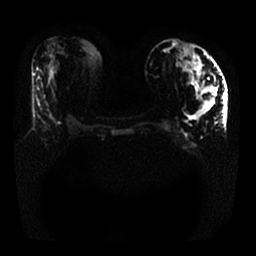
Breast MRI, one axial slice; slice 8 of 25 in the series (ordered by position); diffusion-weighted series; image 2 of 4 stored at this slice position (different b-values; order by instance number); 1.5 T; 4 mm slice thickness; 256 × 256 image matrix, field of view 340 × 340 mm. Female patient.
Annotated regions visible in this slice (manually delineated by an expert):
- tumour on diffusion-weighted imaging: box from (x=197, y=87) to (x=216, y=116) px